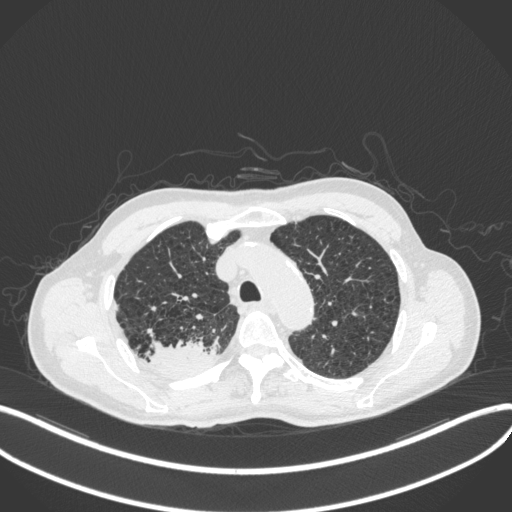
Chest CT, one axial slice; slice 337 of 423 in the series (ordered by position); reconstruction kernel B31f; lung window (W 1500 / L -600 HU); 1 mm slice thickness; 512 × 512 image matrix. Male patient, age 79 years. Case-level facts recorded for this patient, not image findings: clinical TNM (as recorded): T3 N0 M0.
Outlined on this slice (rectangle marked by the reading radiologist):
- lung tumour (recorded histology: adenocarcinoma): bounding box [x1, y1, x2, y2] px = [143, 336, 226, 381]